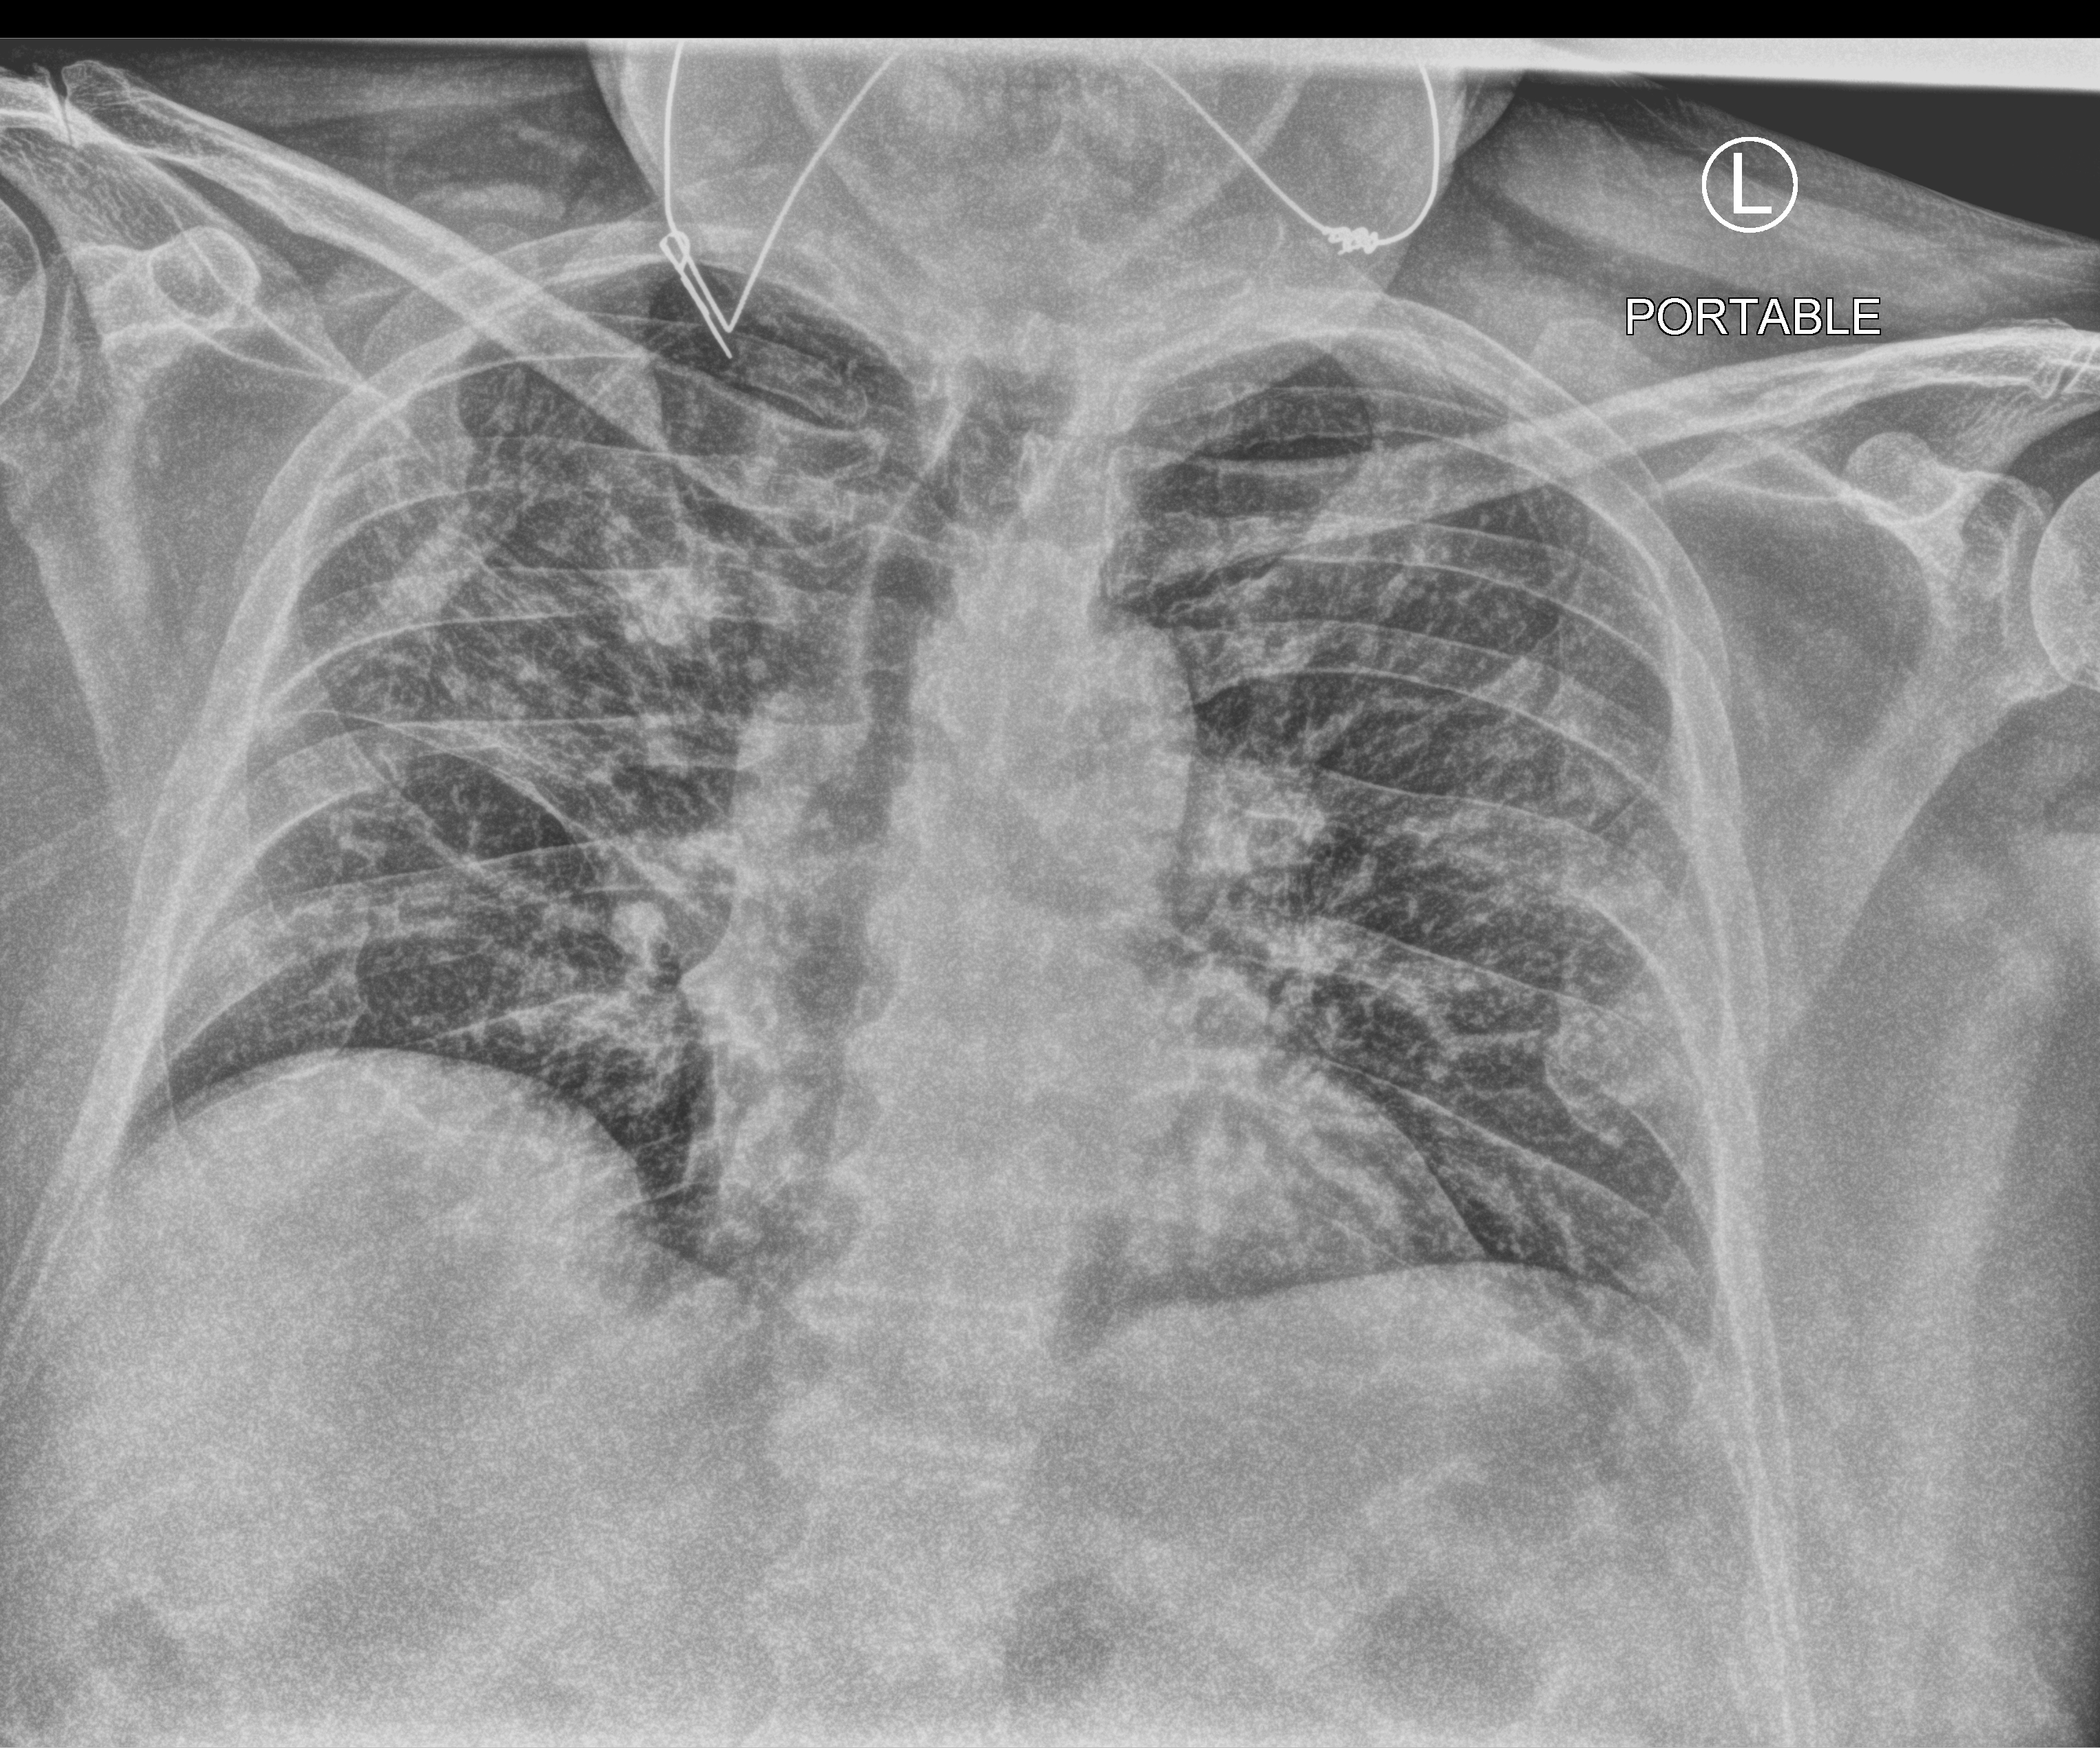
Portable chest radiograph. Male patient hospitalised with COVID-19, age 60–74 years.
Hospital-stay facts (about this admission, not read from this image; timing relative to this image not recorded): COPD (admission record): no.